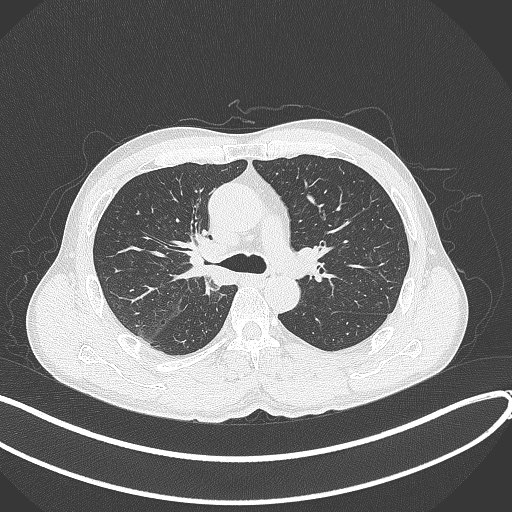
Chest CT, one axial slice. Slice 250 of 409 in the series (ordered by position). Lung window (W 1500 / L -600 HU). 512 × 512 image matrix, field of view 400 × 400 mm. Patient: male, 53 years. Case-level facts recorded for this patient, not image findings: clinical TNM (as recorded): T1b N0 M0.
Structures marked on this image (bounding box drawn by a radiologist):
- lung tumour (recorded histology: squamous cell carcinoma): bounding box <180,226,240,289> (left, top, right, bottom; pixels)